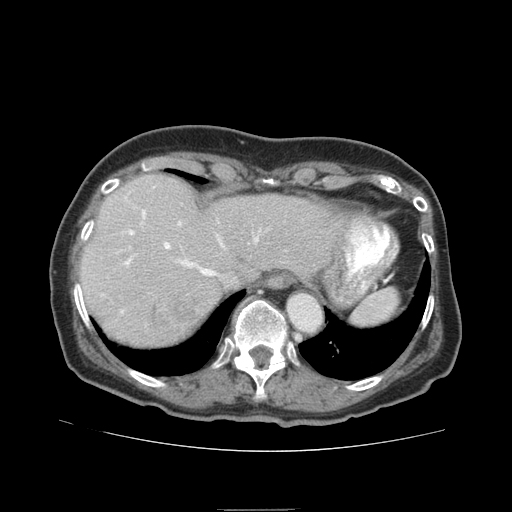
Contrast-enhanced abdominal CT (liver protocol), one axial slice; slice 66 of 95 in the series (ordered by position); reconstruction kernel STANDARD; soft-tissue window (W 400 / L 40 HU); 512 × 512 image matrix, field of view 360 × 360 mm. From the clinical record (not read from this slice): diagnosis: hepatocellular carcinoma (patient treated with transarterial chemoembolisation; whether this scan precedes or follows treatment is not stated here); TNM stage (as recorded): Stage-IVA; Child-Pugh class: B; tumour nodularity: uninodular.
Structures marked on this image (semi-automatic segmentation, software-assisted and operator-edited):
- liver parenchyma outside the tumour (the mass and vessels are separate outlines, so this box may not span the whole liver): bounding box <80,174,346,346> (left, top, right, bottom; pixels)
- mass: <147,292,195,334>
- liver vessels: <121,210,259,313>